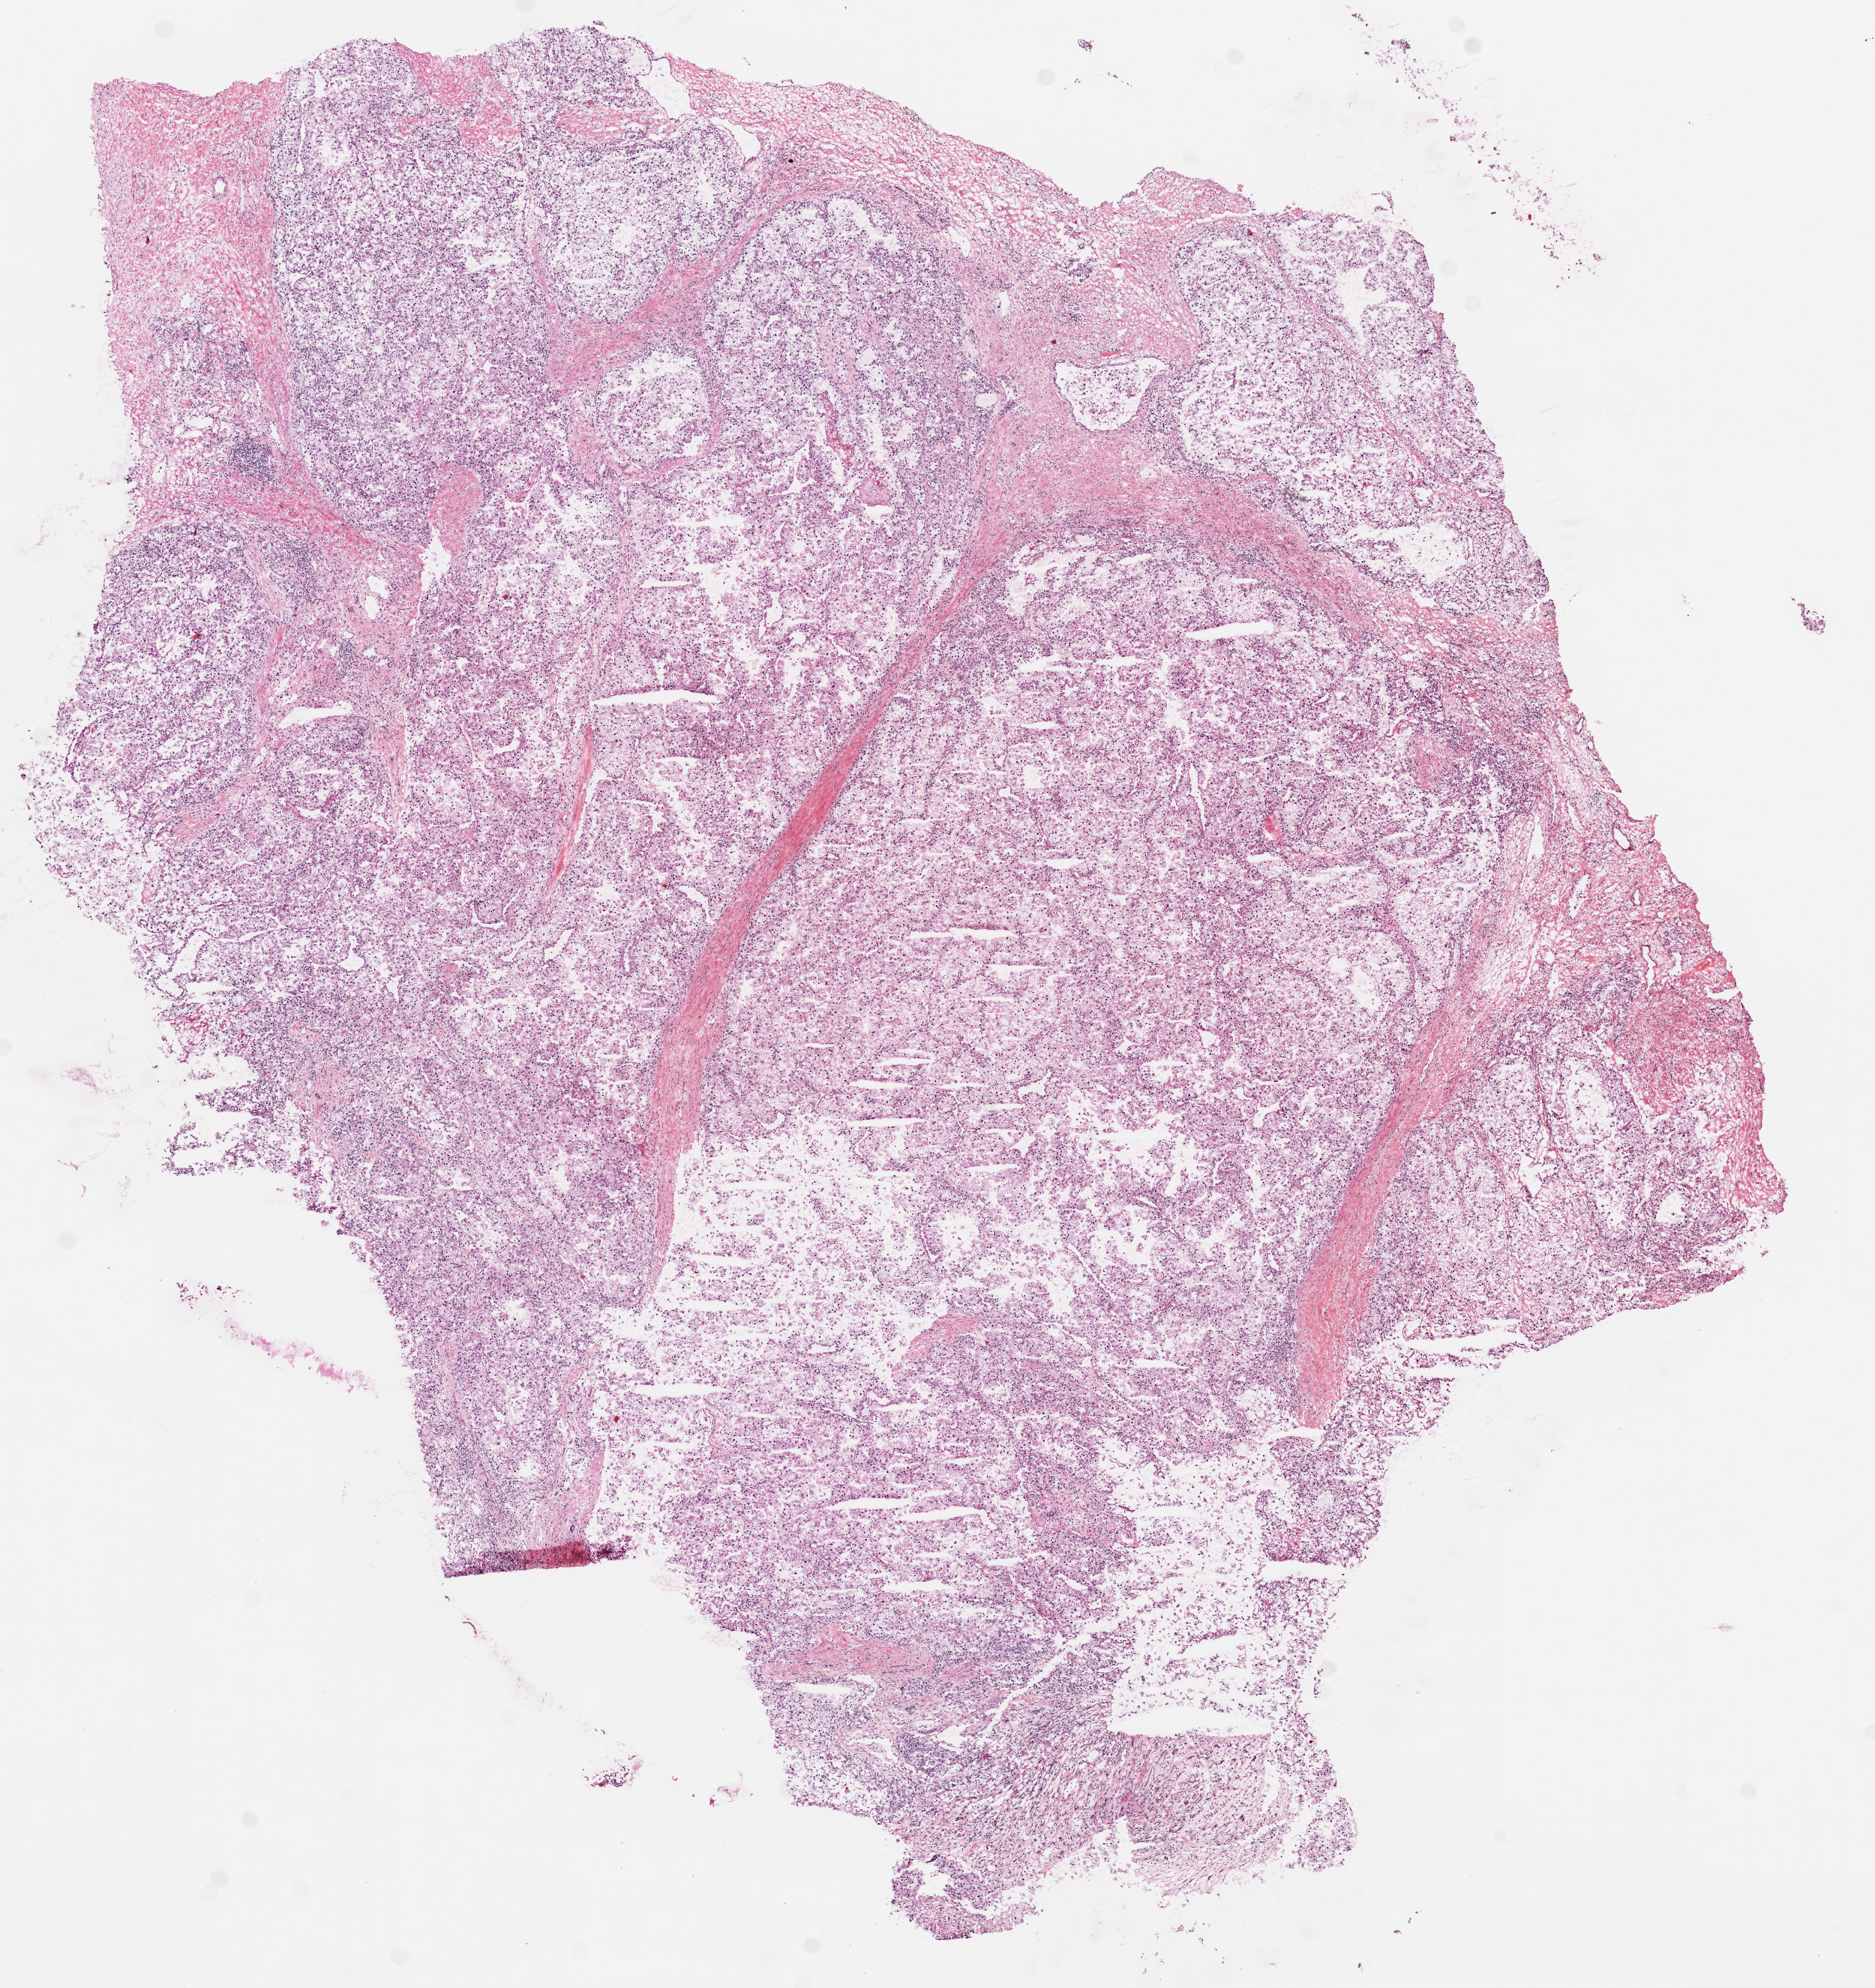
Digitized Hematoxylin and eosin (H&E) stained tissue section (whole slide) — whole scanned area (about 10.0 x 10.6 mm, slide scanned at 20x) shown as a low-resolution overview. Frozen section. Kidney, primary tumour sample. Patient: male, age at initial diagnosis 52 years. Histologic grade: G2 (moderately differentiated). Composition of this section per pathologist review: tumour cells 95%, tumour nuclei 85%, normal cells 0%, stromal cells 5%, necrosis 0%. Infiltration values recorded for this section: lymphocyte infiltration 1%, monocyte infiltration 0%, neutrophil infiltration 0%.
Histologic diagnosis: Clear cell adenocarcinoma, NOS. Lymph nodes positive (case pathology): 2 of 18 examined.